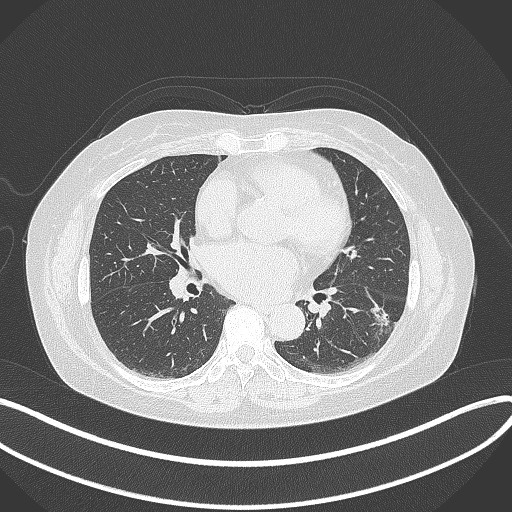
Chest CT, one axial slice. Slice 171 of 373 in the series (ordered by position). Reconstruction kernel B70f. 120 kVp. Lung window (W 1500 / L -600 HU). 1 mm slice thickness. 512 × 512 image matrix. Female patient, age 67 years. Case-level facts recorded for this patient, not image findings: clinical TNM (as recorded): T1c N0 M0; histopathological grade: G2.
Structures marked on this image (bounding box drawn by a radiologist):
- lung tumour (recorded histology: adenocarcinoma): box from (x=362, y=290) to (x=396, y=331) px